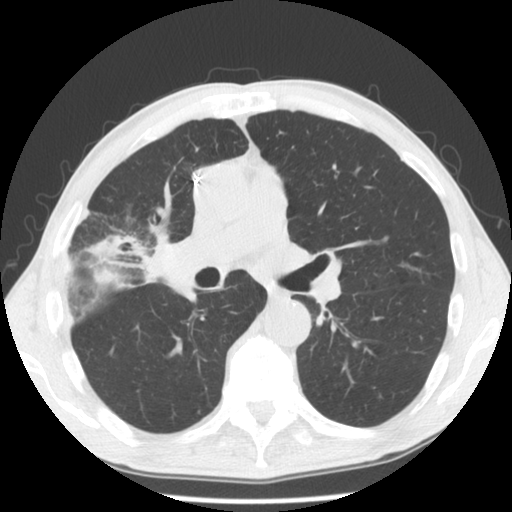
Axial slice from a low-dose chest CT screening exam, third annual screen, lung window (W 1500 / L -600 HU), standard (soft-tissue) reconstruction kernel (STANDARD). Male, age 57 years at enrolment. Former smoker at enrolment.
• Expert-annotated lung lesion, bounding box [x1, y1, x2, y2] px = [58, 206, 165, 303].
• Reader record for this screening exam (exam-level; its link to the box is not recorded): non-calcified nodule or mass ≥4 mm, right upper lobe, 38 × 34 mm, poorly defined margins, mixed attenuation, pre-existing on the prior screen: no.
• Official screen result: positive, other.
• Participant outcome: lung cancer diagnosed 76 days after this screen — squamous cell carcinoma, NOS, right upper lobe, stage IA (AJCC 6th edition), 15 mm at pathology.